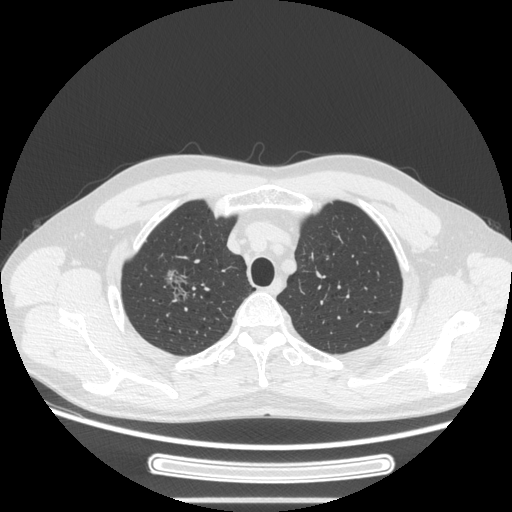
Chest CT, one axial slice. Reconstruction kernel STANDARD. 120 kVp. Lung window (W 1500 / L -600 HU). 512 × 512 image matrix, field of view 382 × 382 mm. Patient: male, 53 years. Case-level facts recorded for this patient, not image findings: clinical TNM (as recorded): T1c N0 M0; histopathological grade: G2.
Outlined on this slice (bounding box drawn by a radiologist):
- lung tumour (recorded histology: adenocarcinoma): bounding box (x1, y1, x2, y2) in pixels: (163, 267, 193, 309)